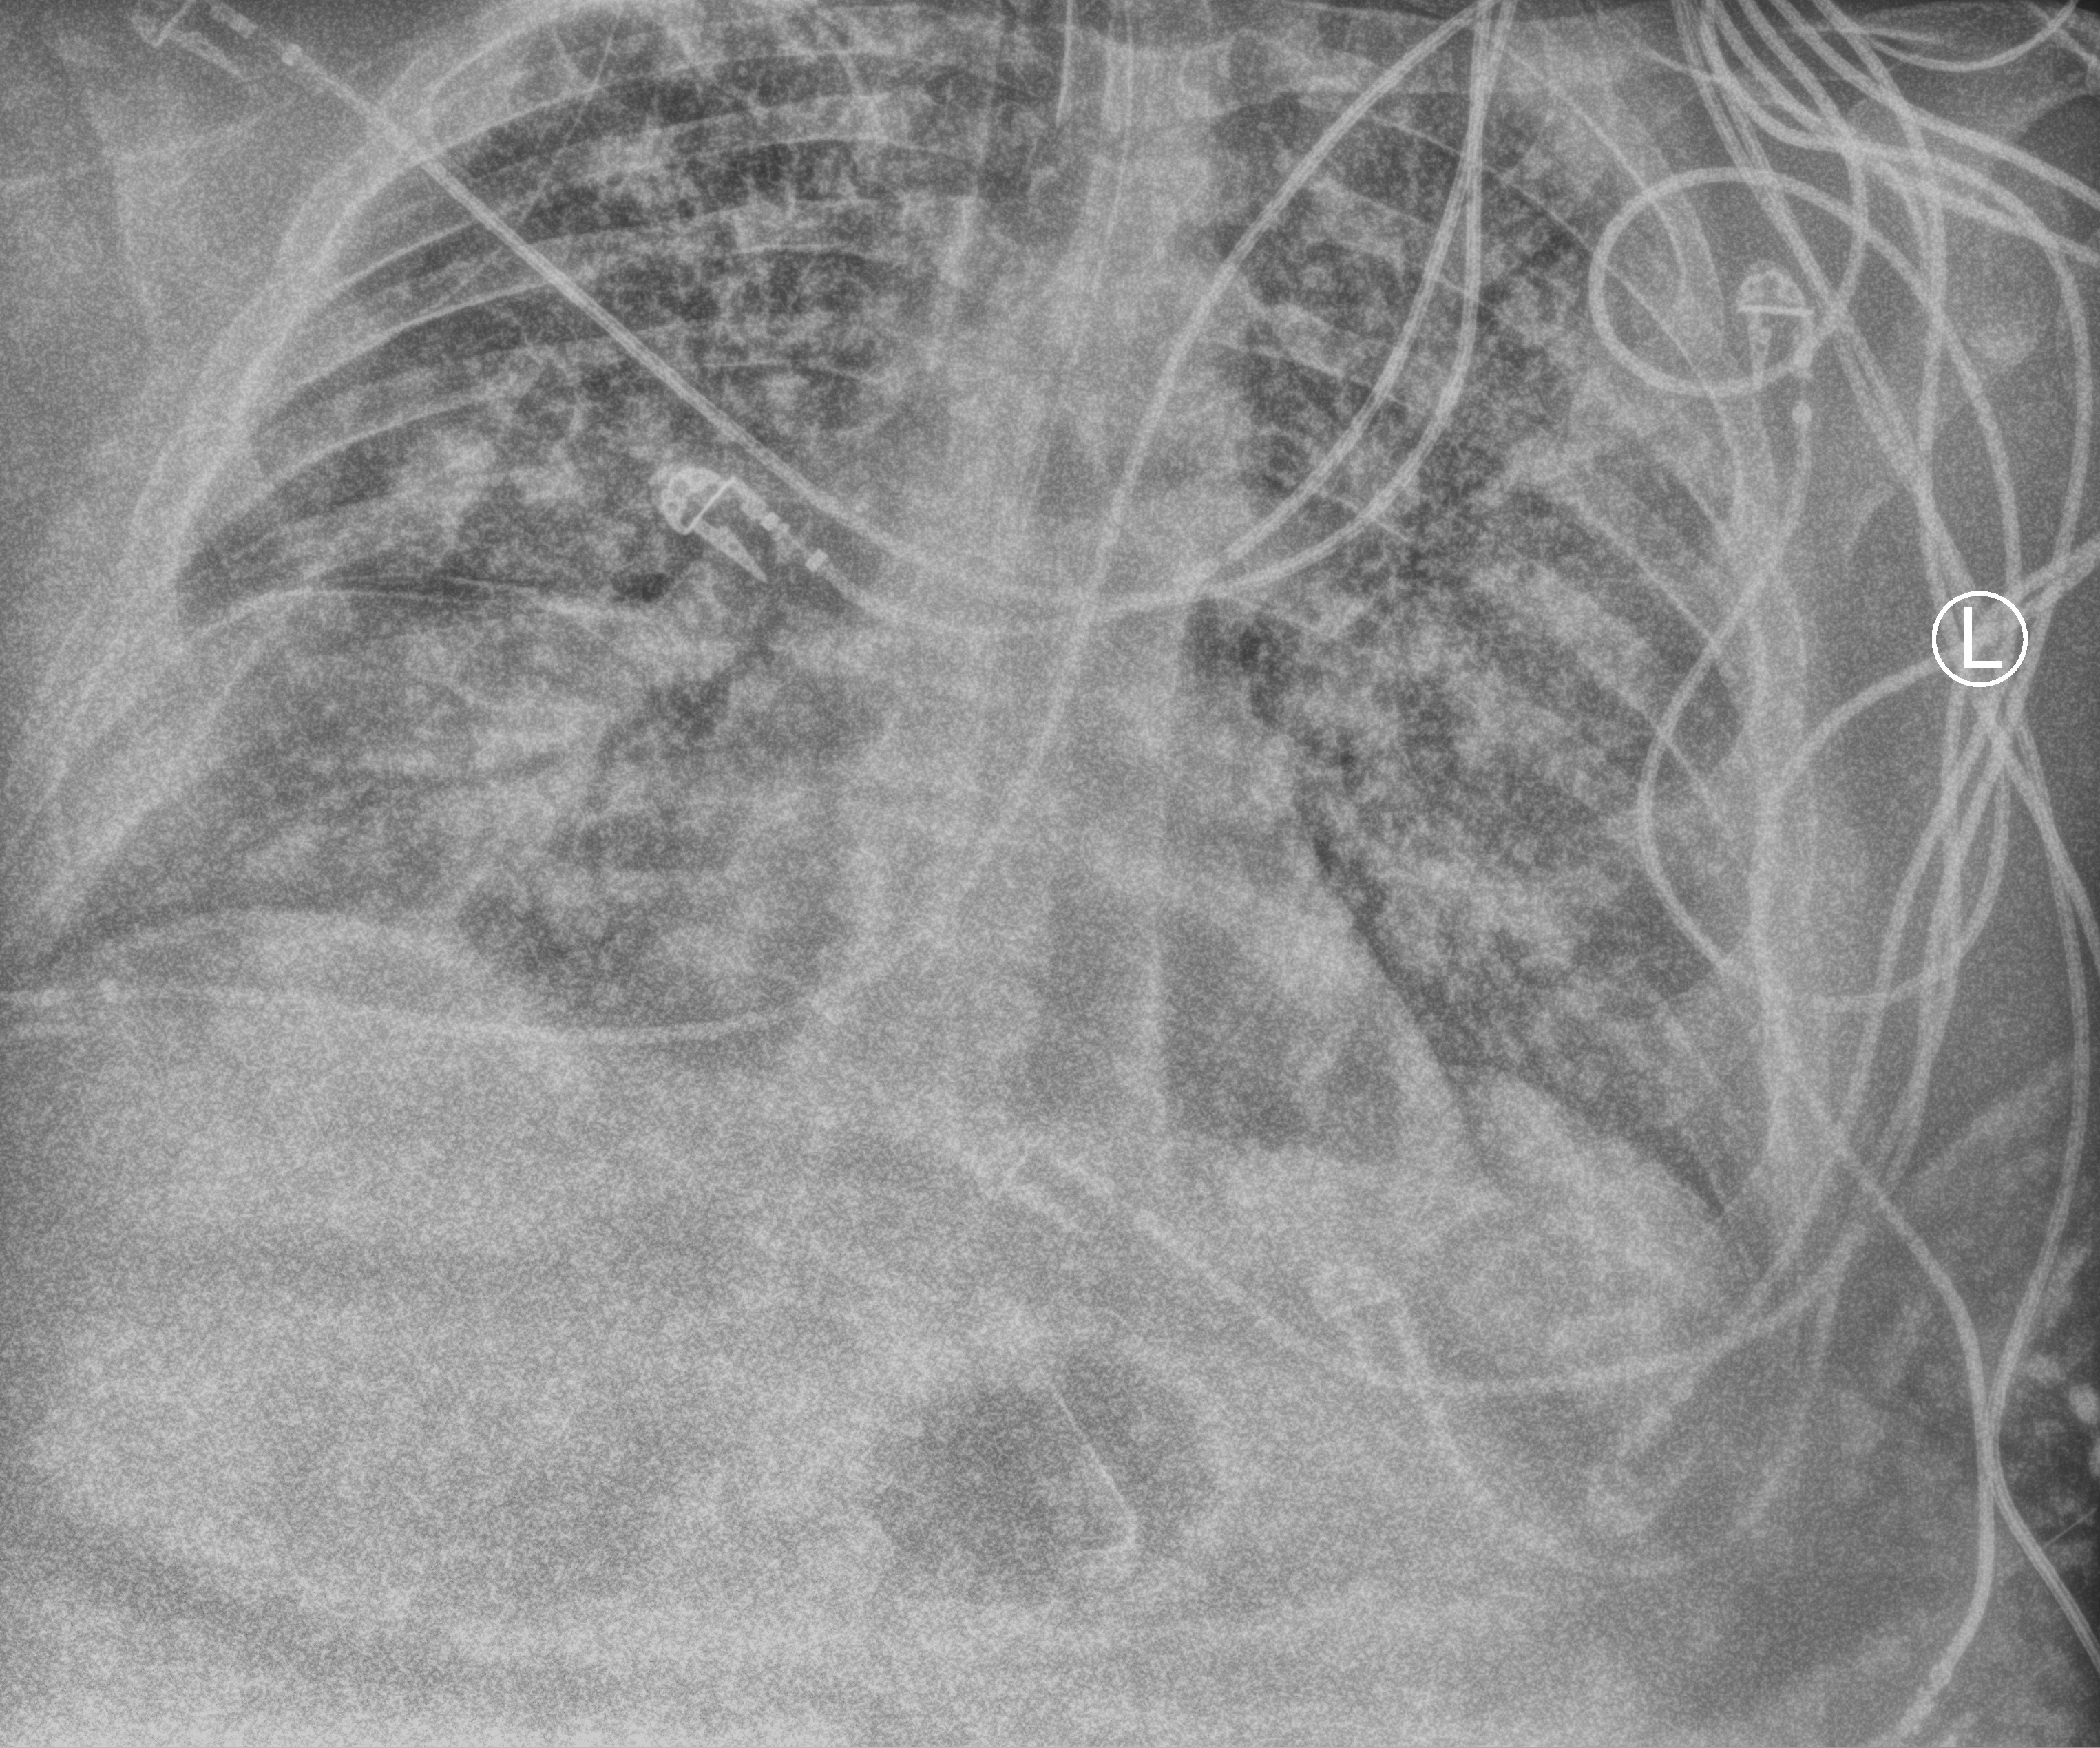
Portable chest radiograph, anteroposterior (AP) projection. Male patient hospitalised with COVID-19, age 60–74 years.
Hospital-stay facts (about this admission, not read from this image; timing relative to this image not recorded): mechanically ventilated during this hospital stay: yes.